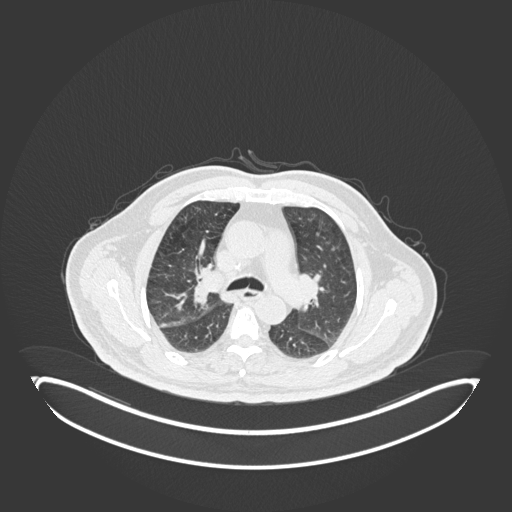
Chest CT, one axial slice; slice 118 of 247 in the series (ordered by position); reconstruction kernel B30f; lung window (W 1500 / L -600 HU); 1 mm slice thickness; 512 × 512 image matrix, field of view 500 × 500 mm. Patient: male, 72 years. Case-level facts recorded for this patient, not image findings: clinical TNM (as recorded): T1c N0 M0; histopathological grade: G2.
Outlined on this slice (bounding box drawn by a radiologist):
- lung tumour (recorded histology: squamous cell carcinoma): box from (x=188, y=264) to (x=218, y=308) px